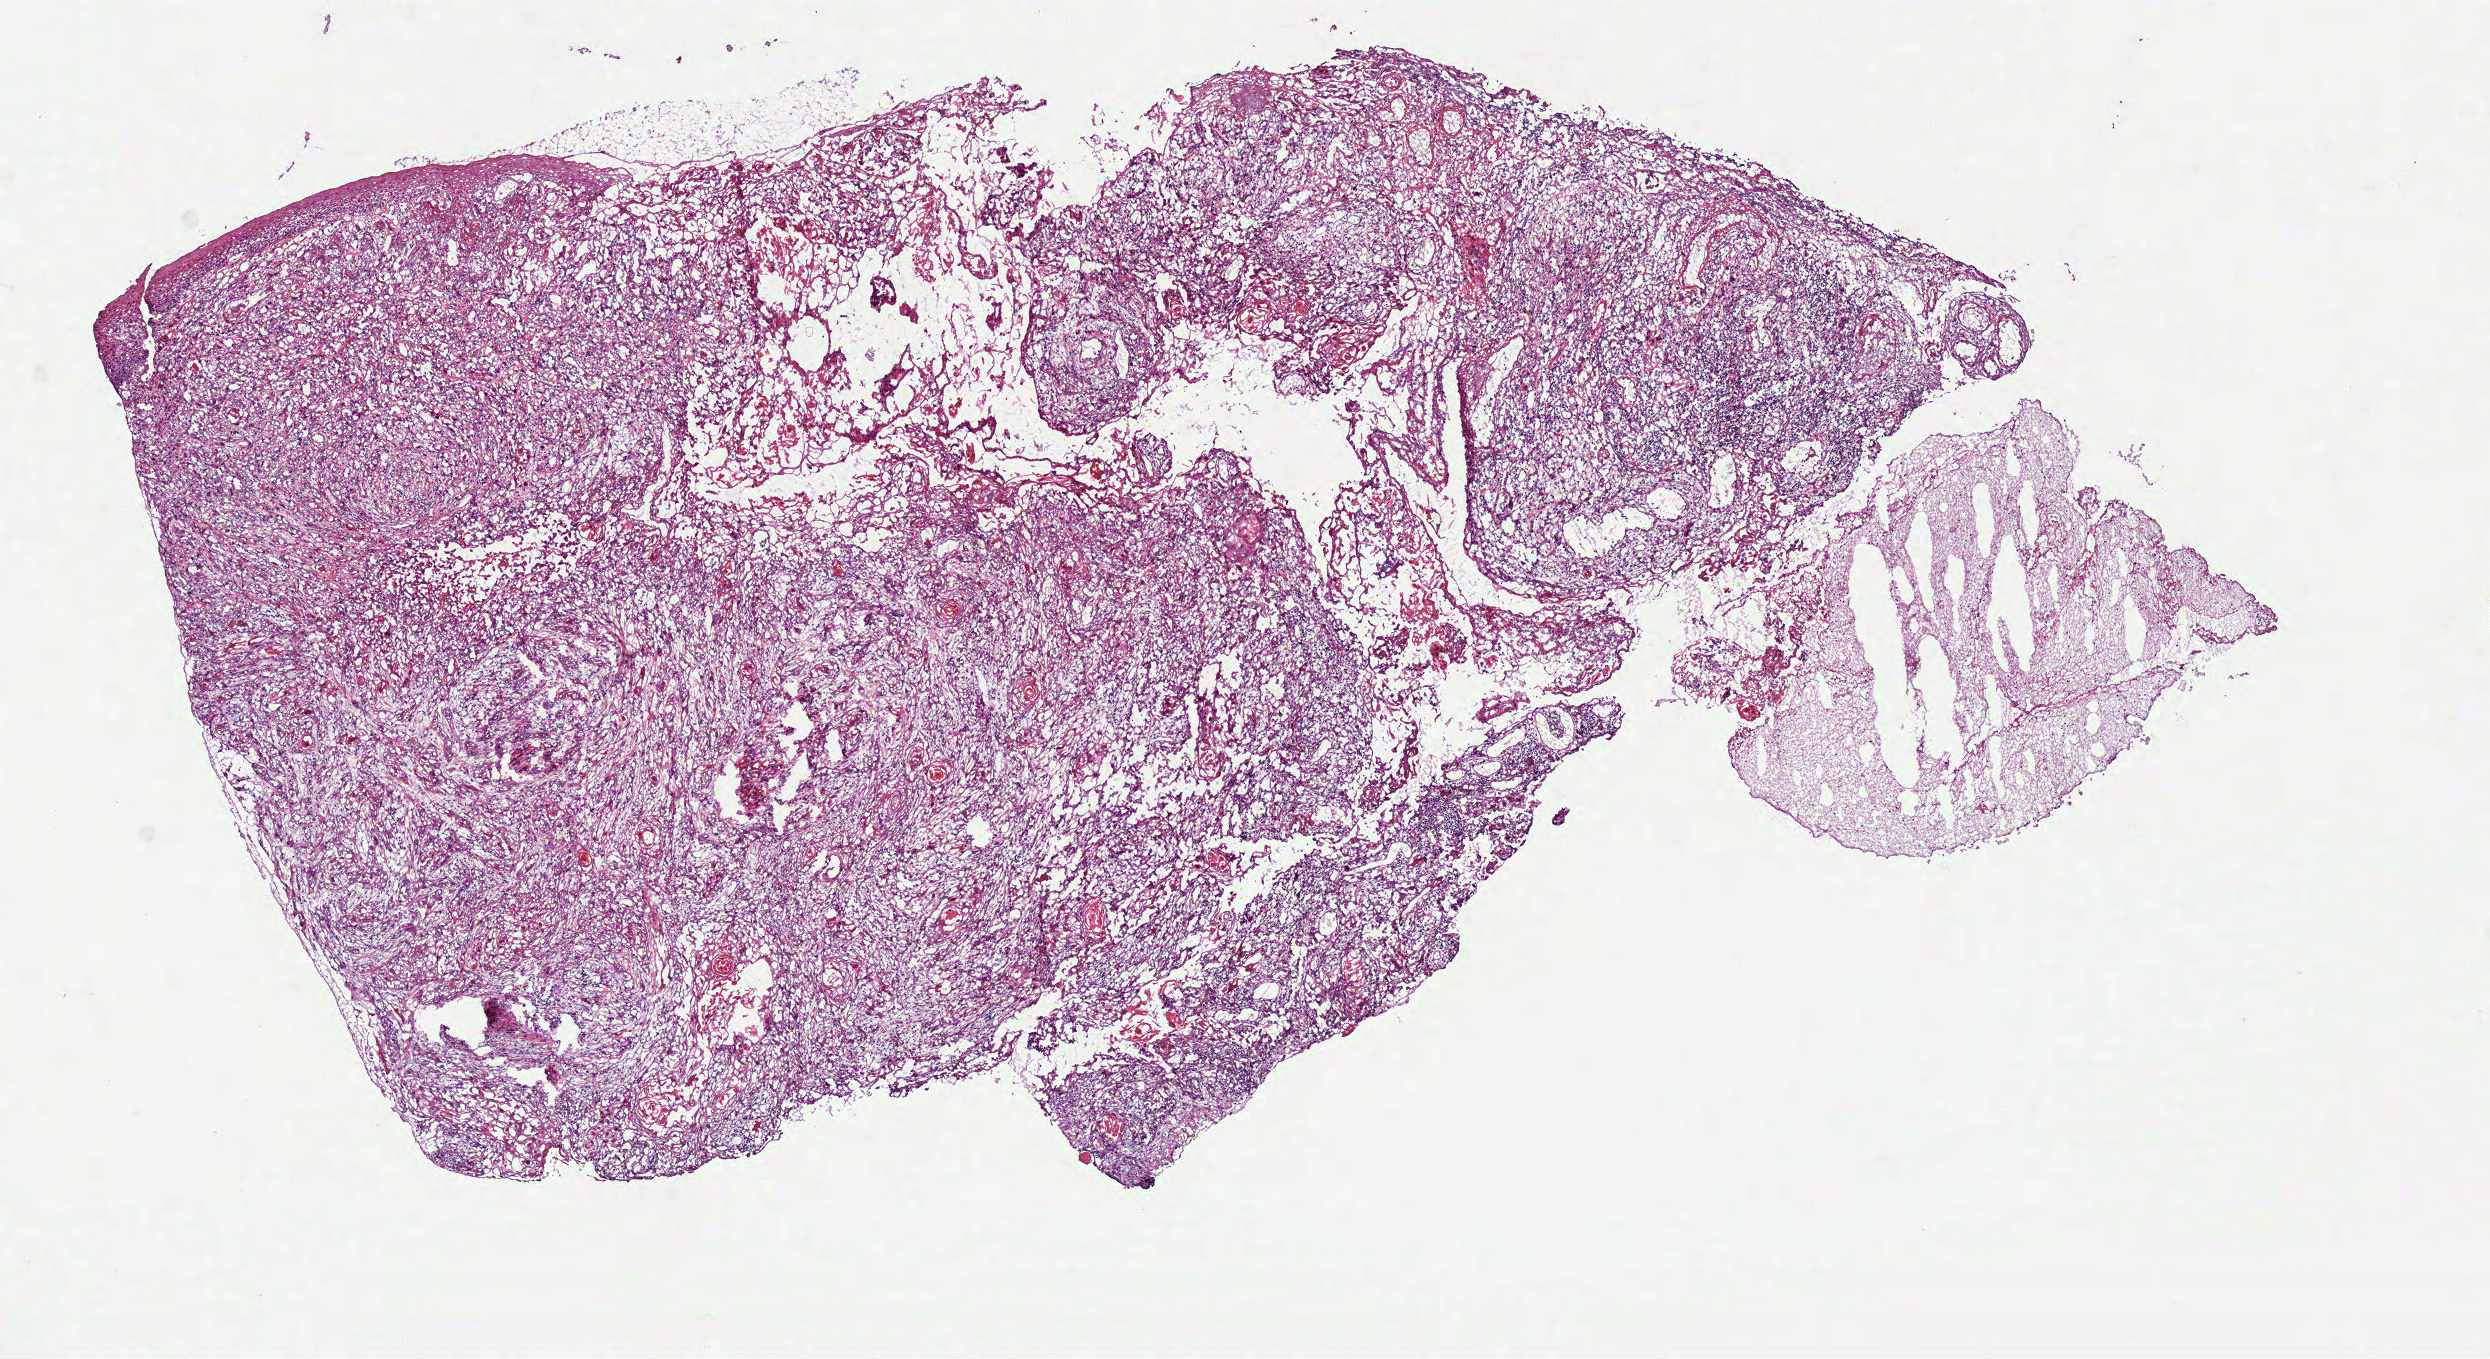
Digitized Hematoxylin and eosin (H&E) stained tissue section (whole slide) — whole scanned area (about 9.8 x 5.3 mm) shown as a low-resolution overview. Frozen section from the bottom of the tissue portion. Head and neck, primary tumour sample. Patient: female, age at initial diagnosis 43 years. Histologic grade: G2 (moderately differentiated). Slide review estimates, as recorded: tumour cells 83%, tumour nuclei 75%, normal cells 5%, stromal cells 1%, necrosis 1%. Infiltration values recorded for this section: lymphocyte infiltration 10%, monocyte infiltration 0%, neutrophil infiltration 0%.
Diagnosis: Squamous cell carcinoma, NOS (tongue, NOS). Laterality: right.